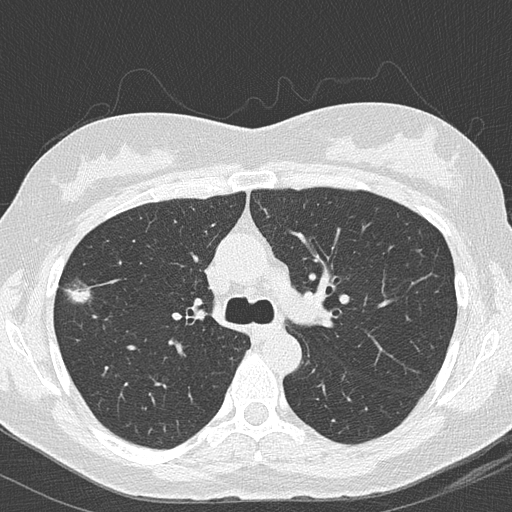
Low-dose screening chest CT, axial slice; second screening round (one year after baseline); lung window (W 1500 / L -600 HU); slice 49 of 157 in the series. Female participant, aged 64 years at enrolment.
Lesion marked by an expert reader, bounding box [x1, y1, x2, y2] px = [48, 267, 104, 317]. The exam's reader record, not a measurement of the box and not confirmed to be the same lesion: non-calcified nodule or mass ≥4 mm, right upper lobe, 16 × 13 mm, mixed attenuation, pre-existing on the prior screen: yes; interval growth: yes. Official screen result: positive, other. Participant outcome: lung cancer diagnosed 112 days after this screen — bronchiolo-alveolar adenocarcinoma, NOS, right upper lobe, well differentiated (G1), stage IA (AJCC 6th edition), 10 mm at pathology.